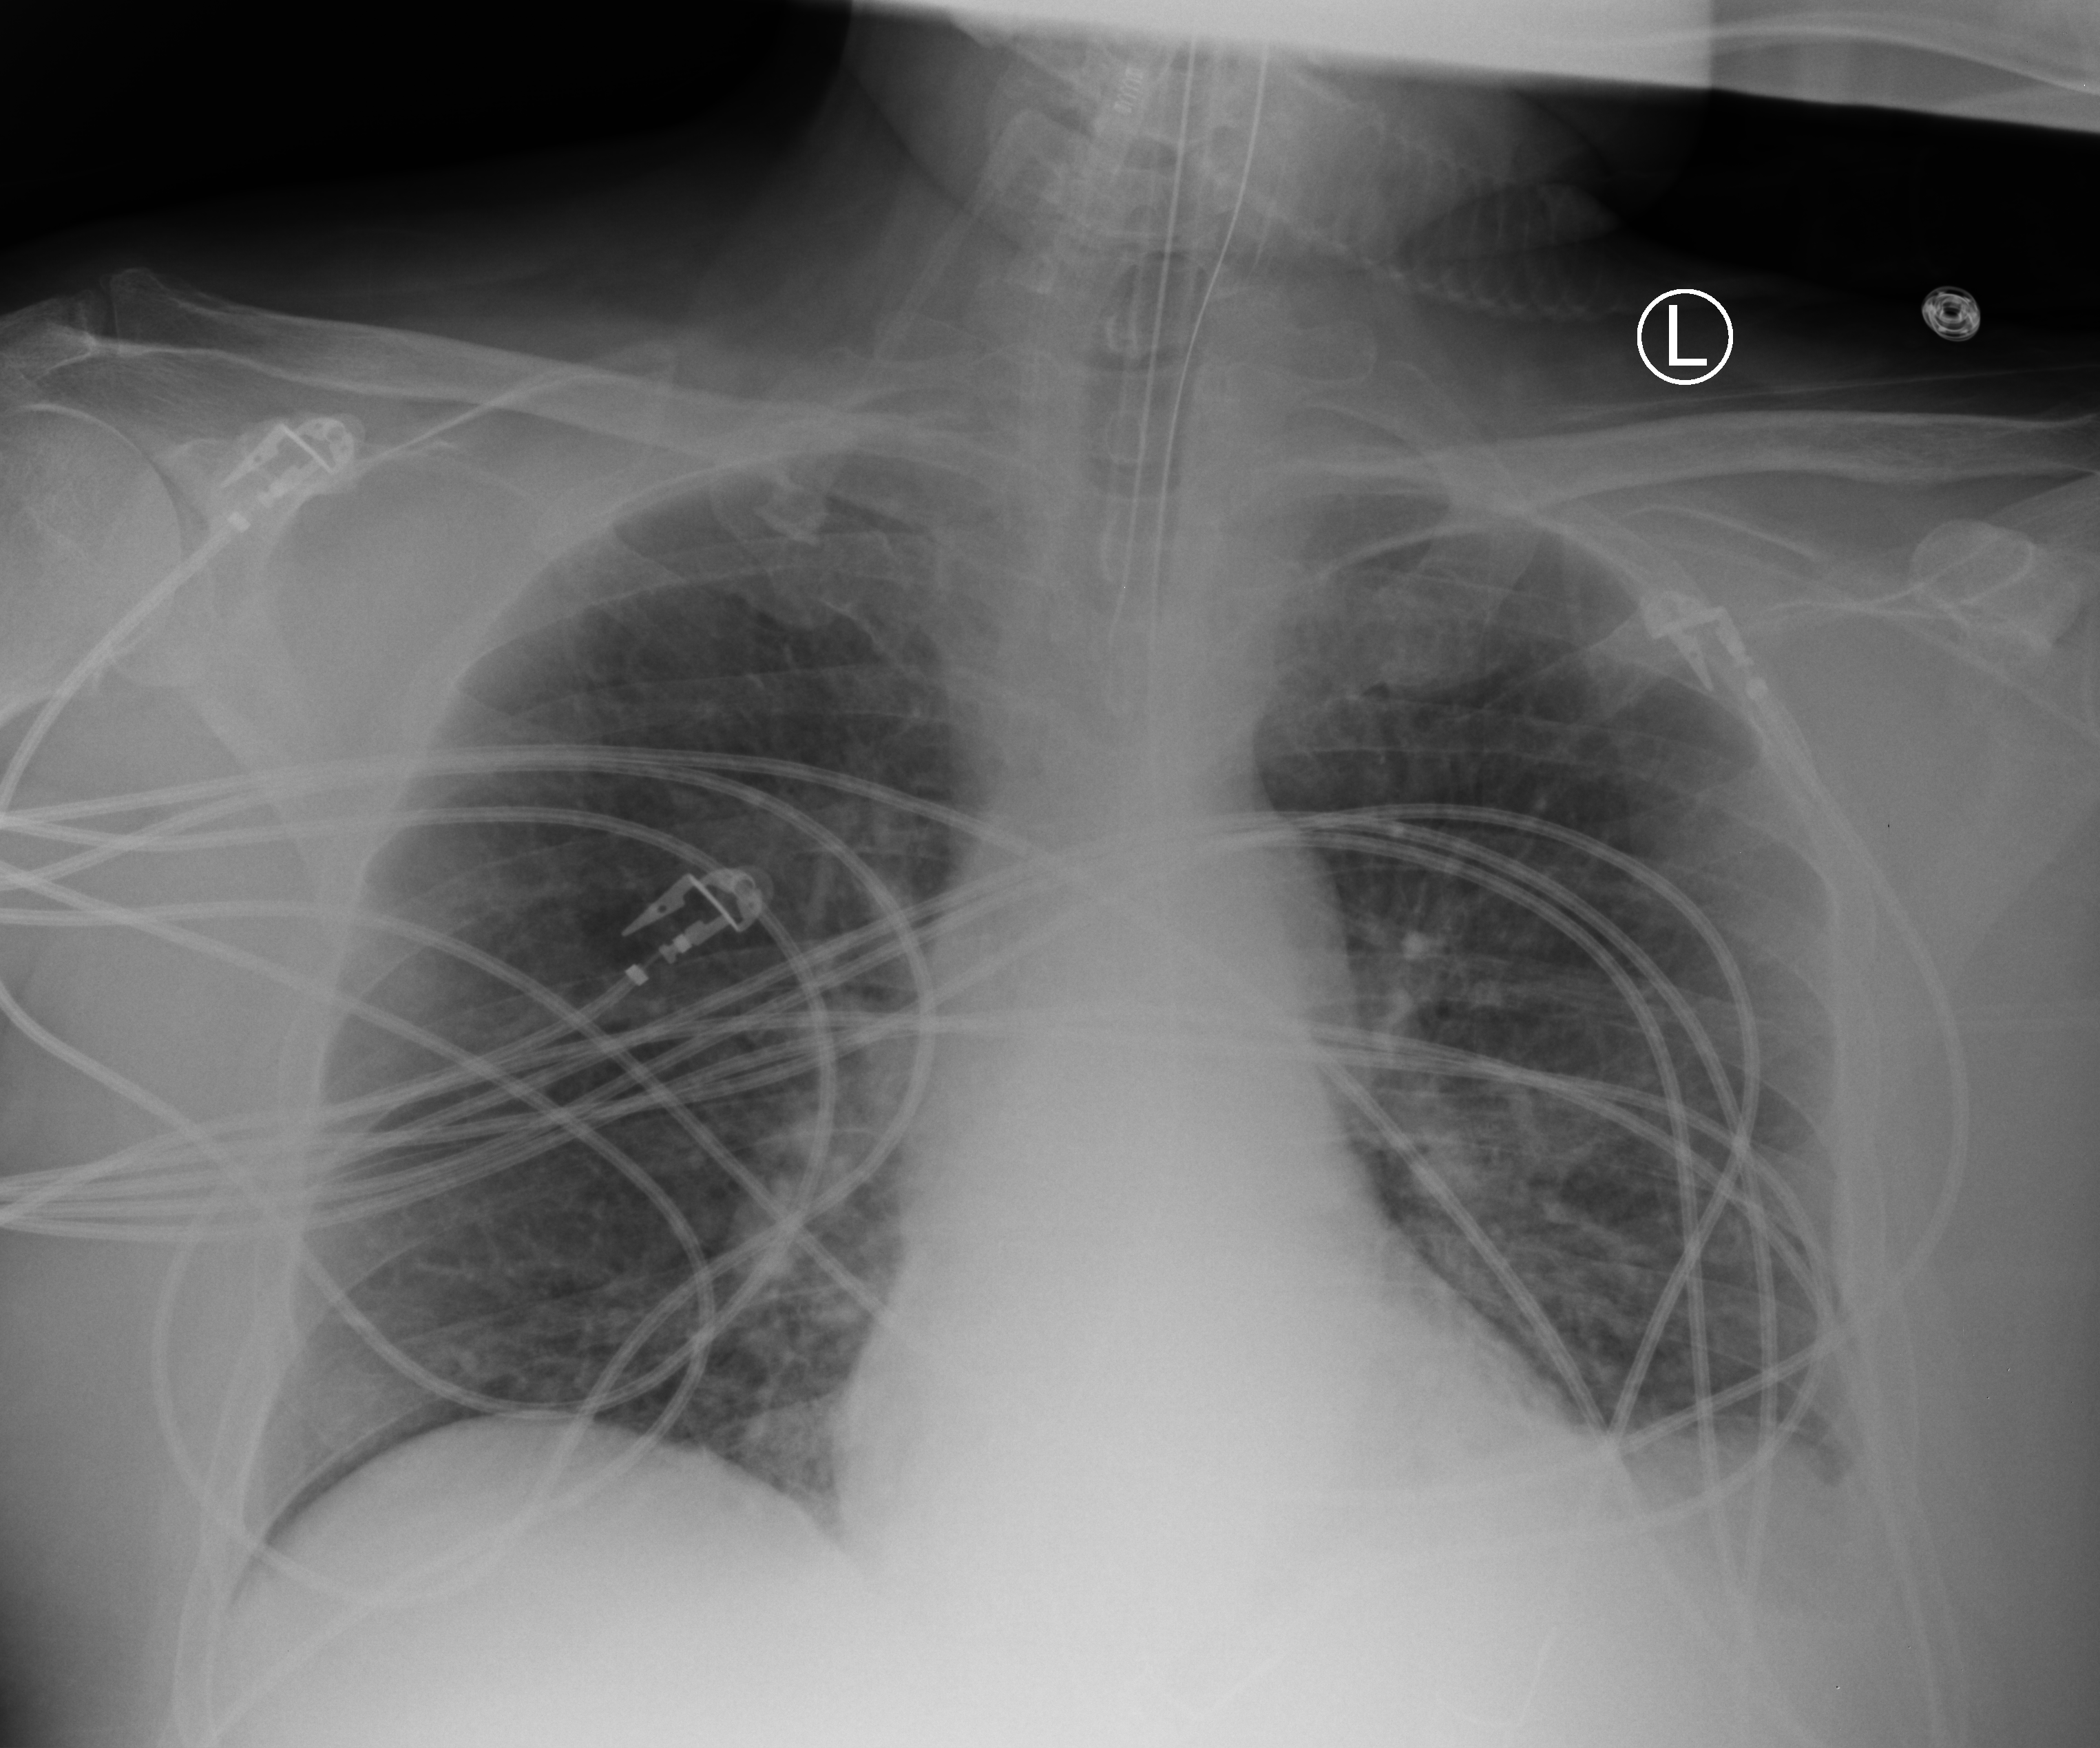
Portable chest radiograph. Male patient hospitalised with COVID-19, age 60–74 years.
From the hospital-stay record, not from the radiograph (when in the stay this image was taken is not recorded):
- mechanically ventilated during this hospital stay: yes